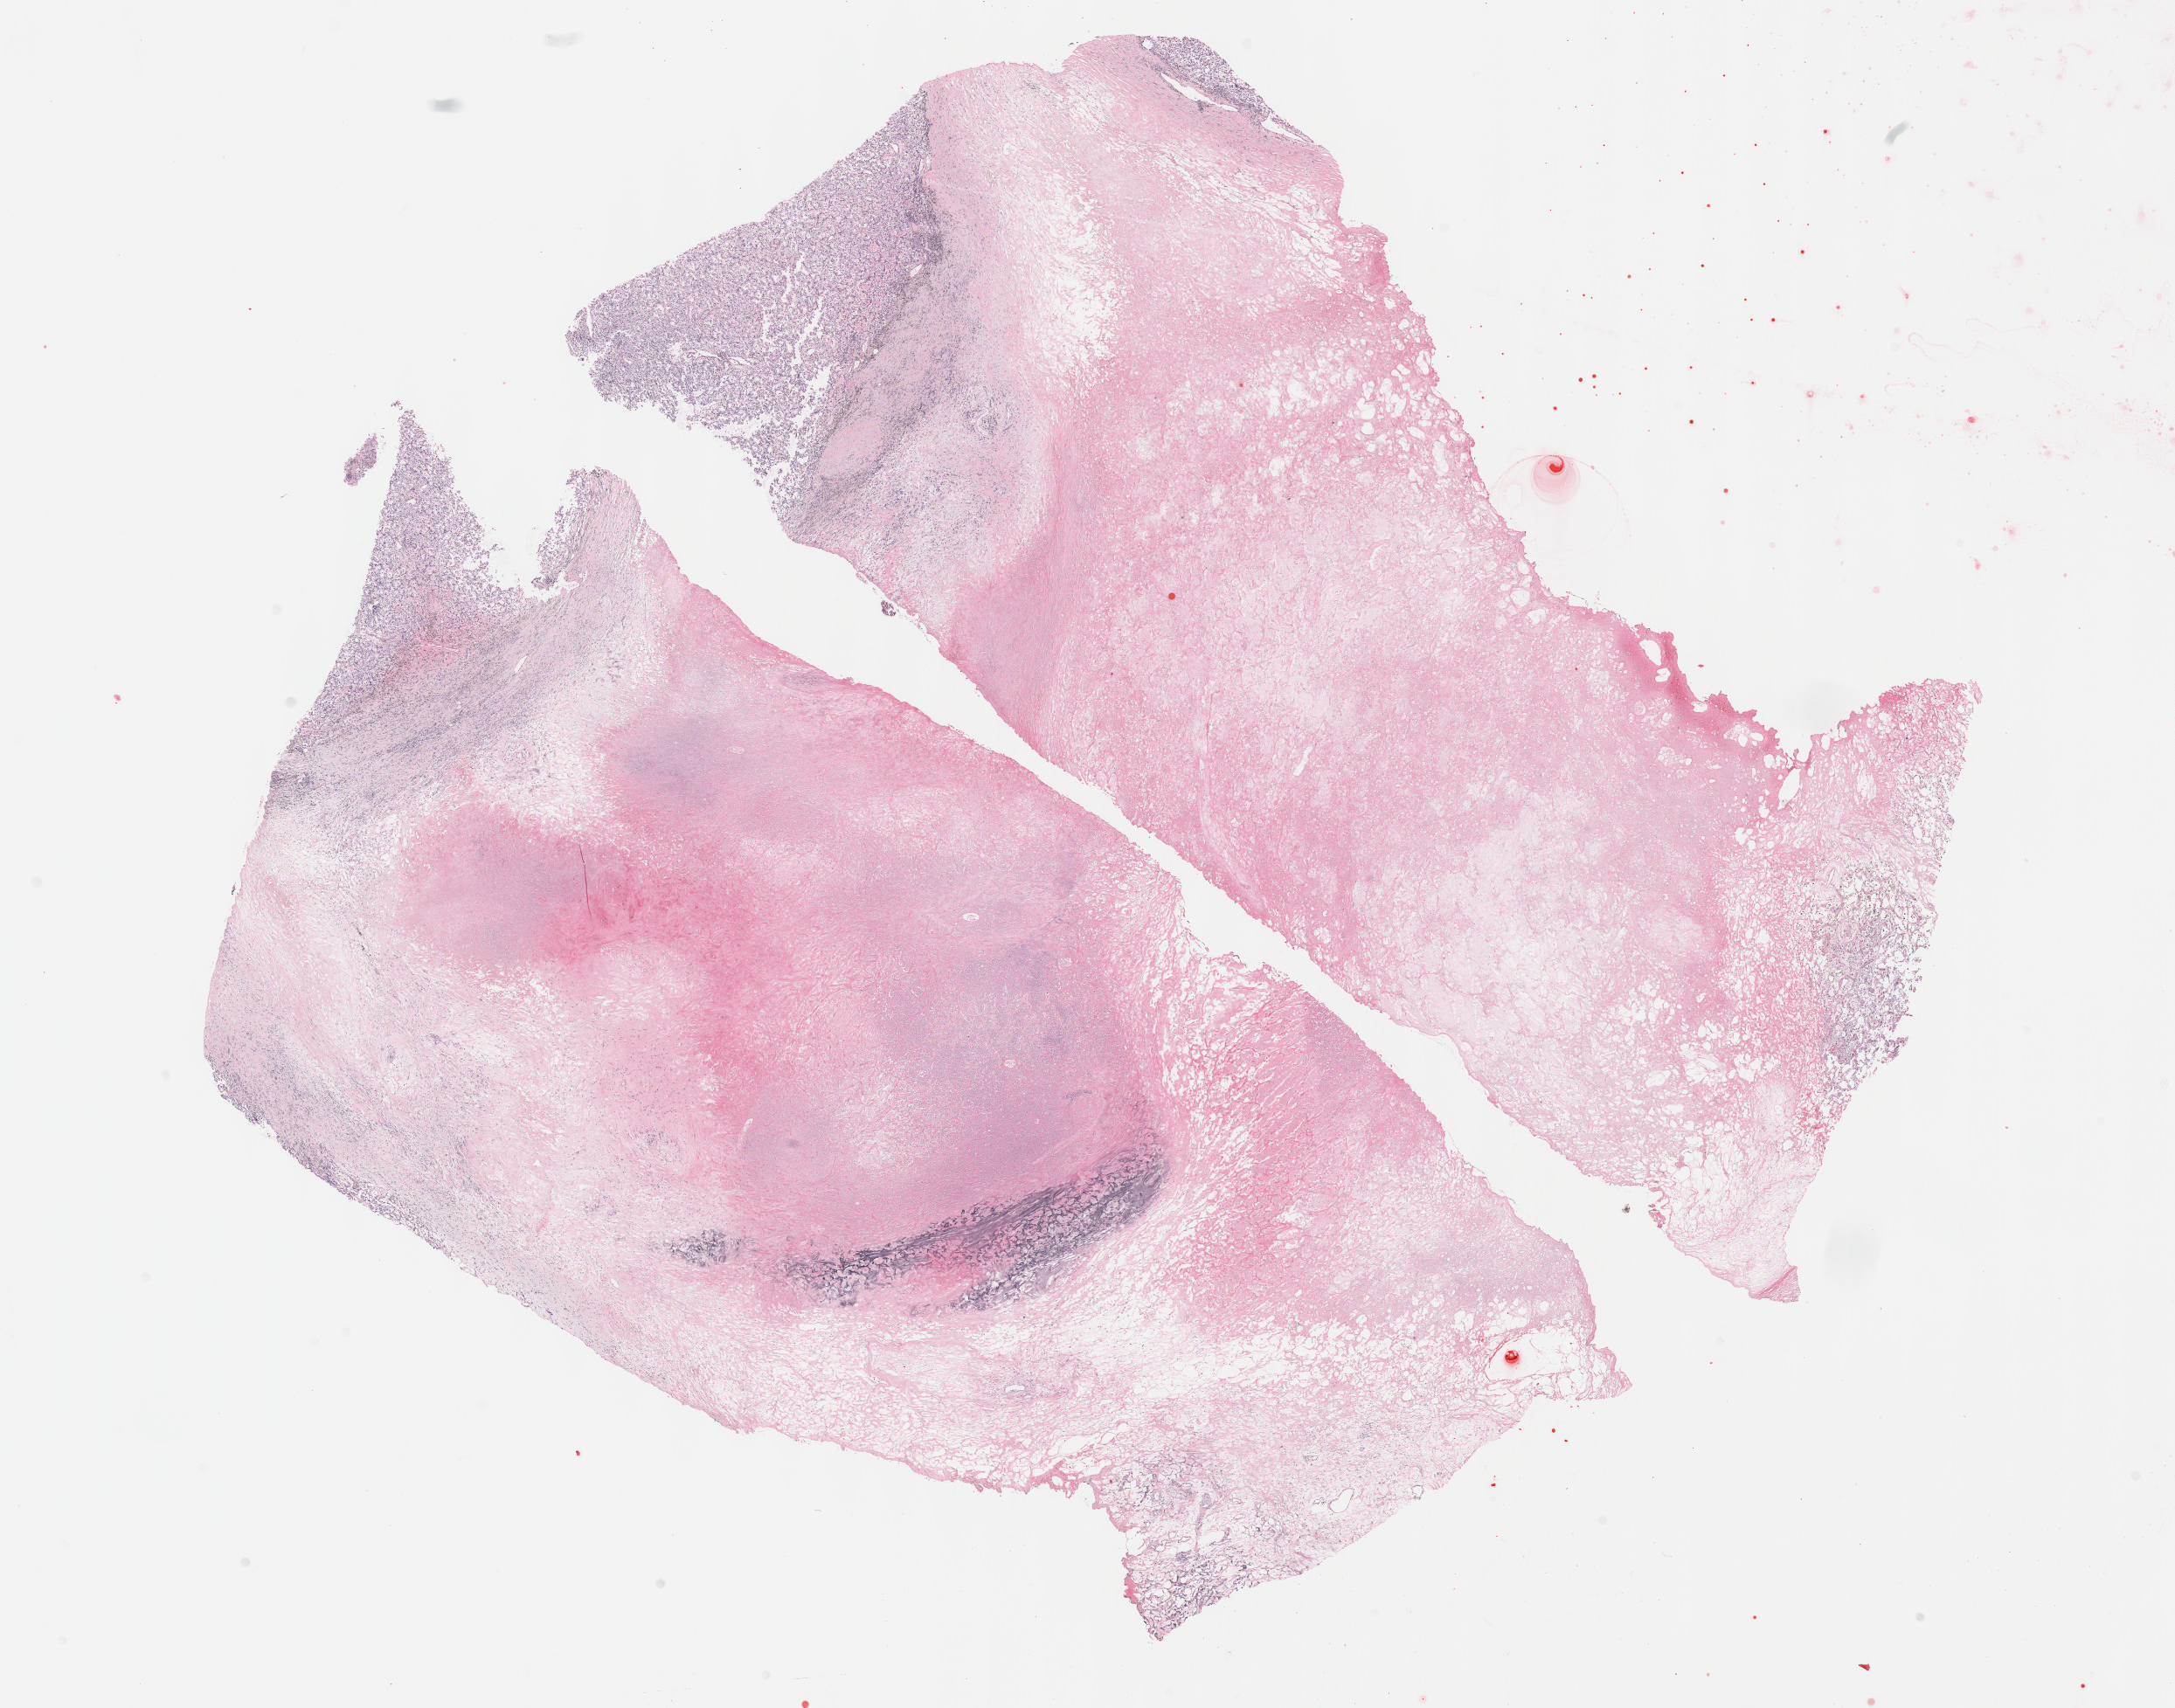
Whole-slide histology image, Hematoxylin and eosin (H&E) stained, shown as a low-resolution overview of the whole scanned area (about 20.1 x 15.8 mm), formalin-fixed paraffin-embedded (FFPE) diagnostic section, sample: primary tumour, kidney. Male, age 69 years at initial diagnosis. Histologic grade: G3 (poorly differentiated).
AJCC pathologic stage: III (6th edition). Laterality: left. Diagnosis: Clear cell adenocarcinoma, NOS.